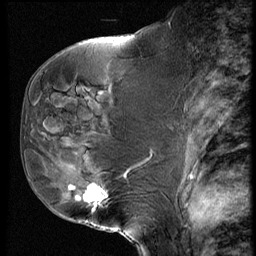
Breast MRI (dynamic contrast-enhanced), one sagittal slice. Slice 30 of 60 in the series (ordered by position). Dynamic contrast-enhanced series, image 2 of 4 at this slice position (ordered by acquisition). 1.5 T. TE 4.2 ms, TR 9 ms. 256 × 256 image matrix, field of view 180 × 180 mm. Female patient, age 50 years. Case-level facts recorded for this patient, not image findings: setting: breast cancer imaged before/during neoadjuvant chemotherapy; receptor status: HR-positive, HER2-negative.
Structures marked on this image (semi-automatic segmentation, software-assisted and operator-edited):
- analysis volume of interest (the breast-tissue region the enhancement analysis was run in; not a lesion): box from (x=48, y=109) to (x=135, y=230) px
- tumour enhancement mask (voxels above the 140 % enhancement threshold inside the analysis volume of interest): (x=84, y=186)–(x=108, y=206)